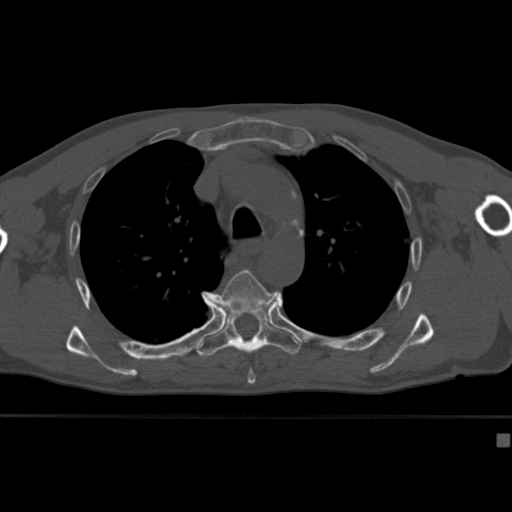
CT including the spine, one axial slice. Slice 301 of 430 in the series (ordered by position). Reconstruction kernel Br40s. 120 kVp. Bone window (W 1800 / L 400 HU). 512 × 512 image matrix, field of view 337 × 337 mm. Patient: male, 64 years. From the clinical record (not read from this slice): primary cancer: uterus.
Annotated regions visible in this slice (semi-automatic segmentation, software-assisted and operator-edited):
- T5 vertebra: bounding box <210,270,280,382> (left, top, right, bottom; pixels)
- T6 vertebra: <197,308,301,360>